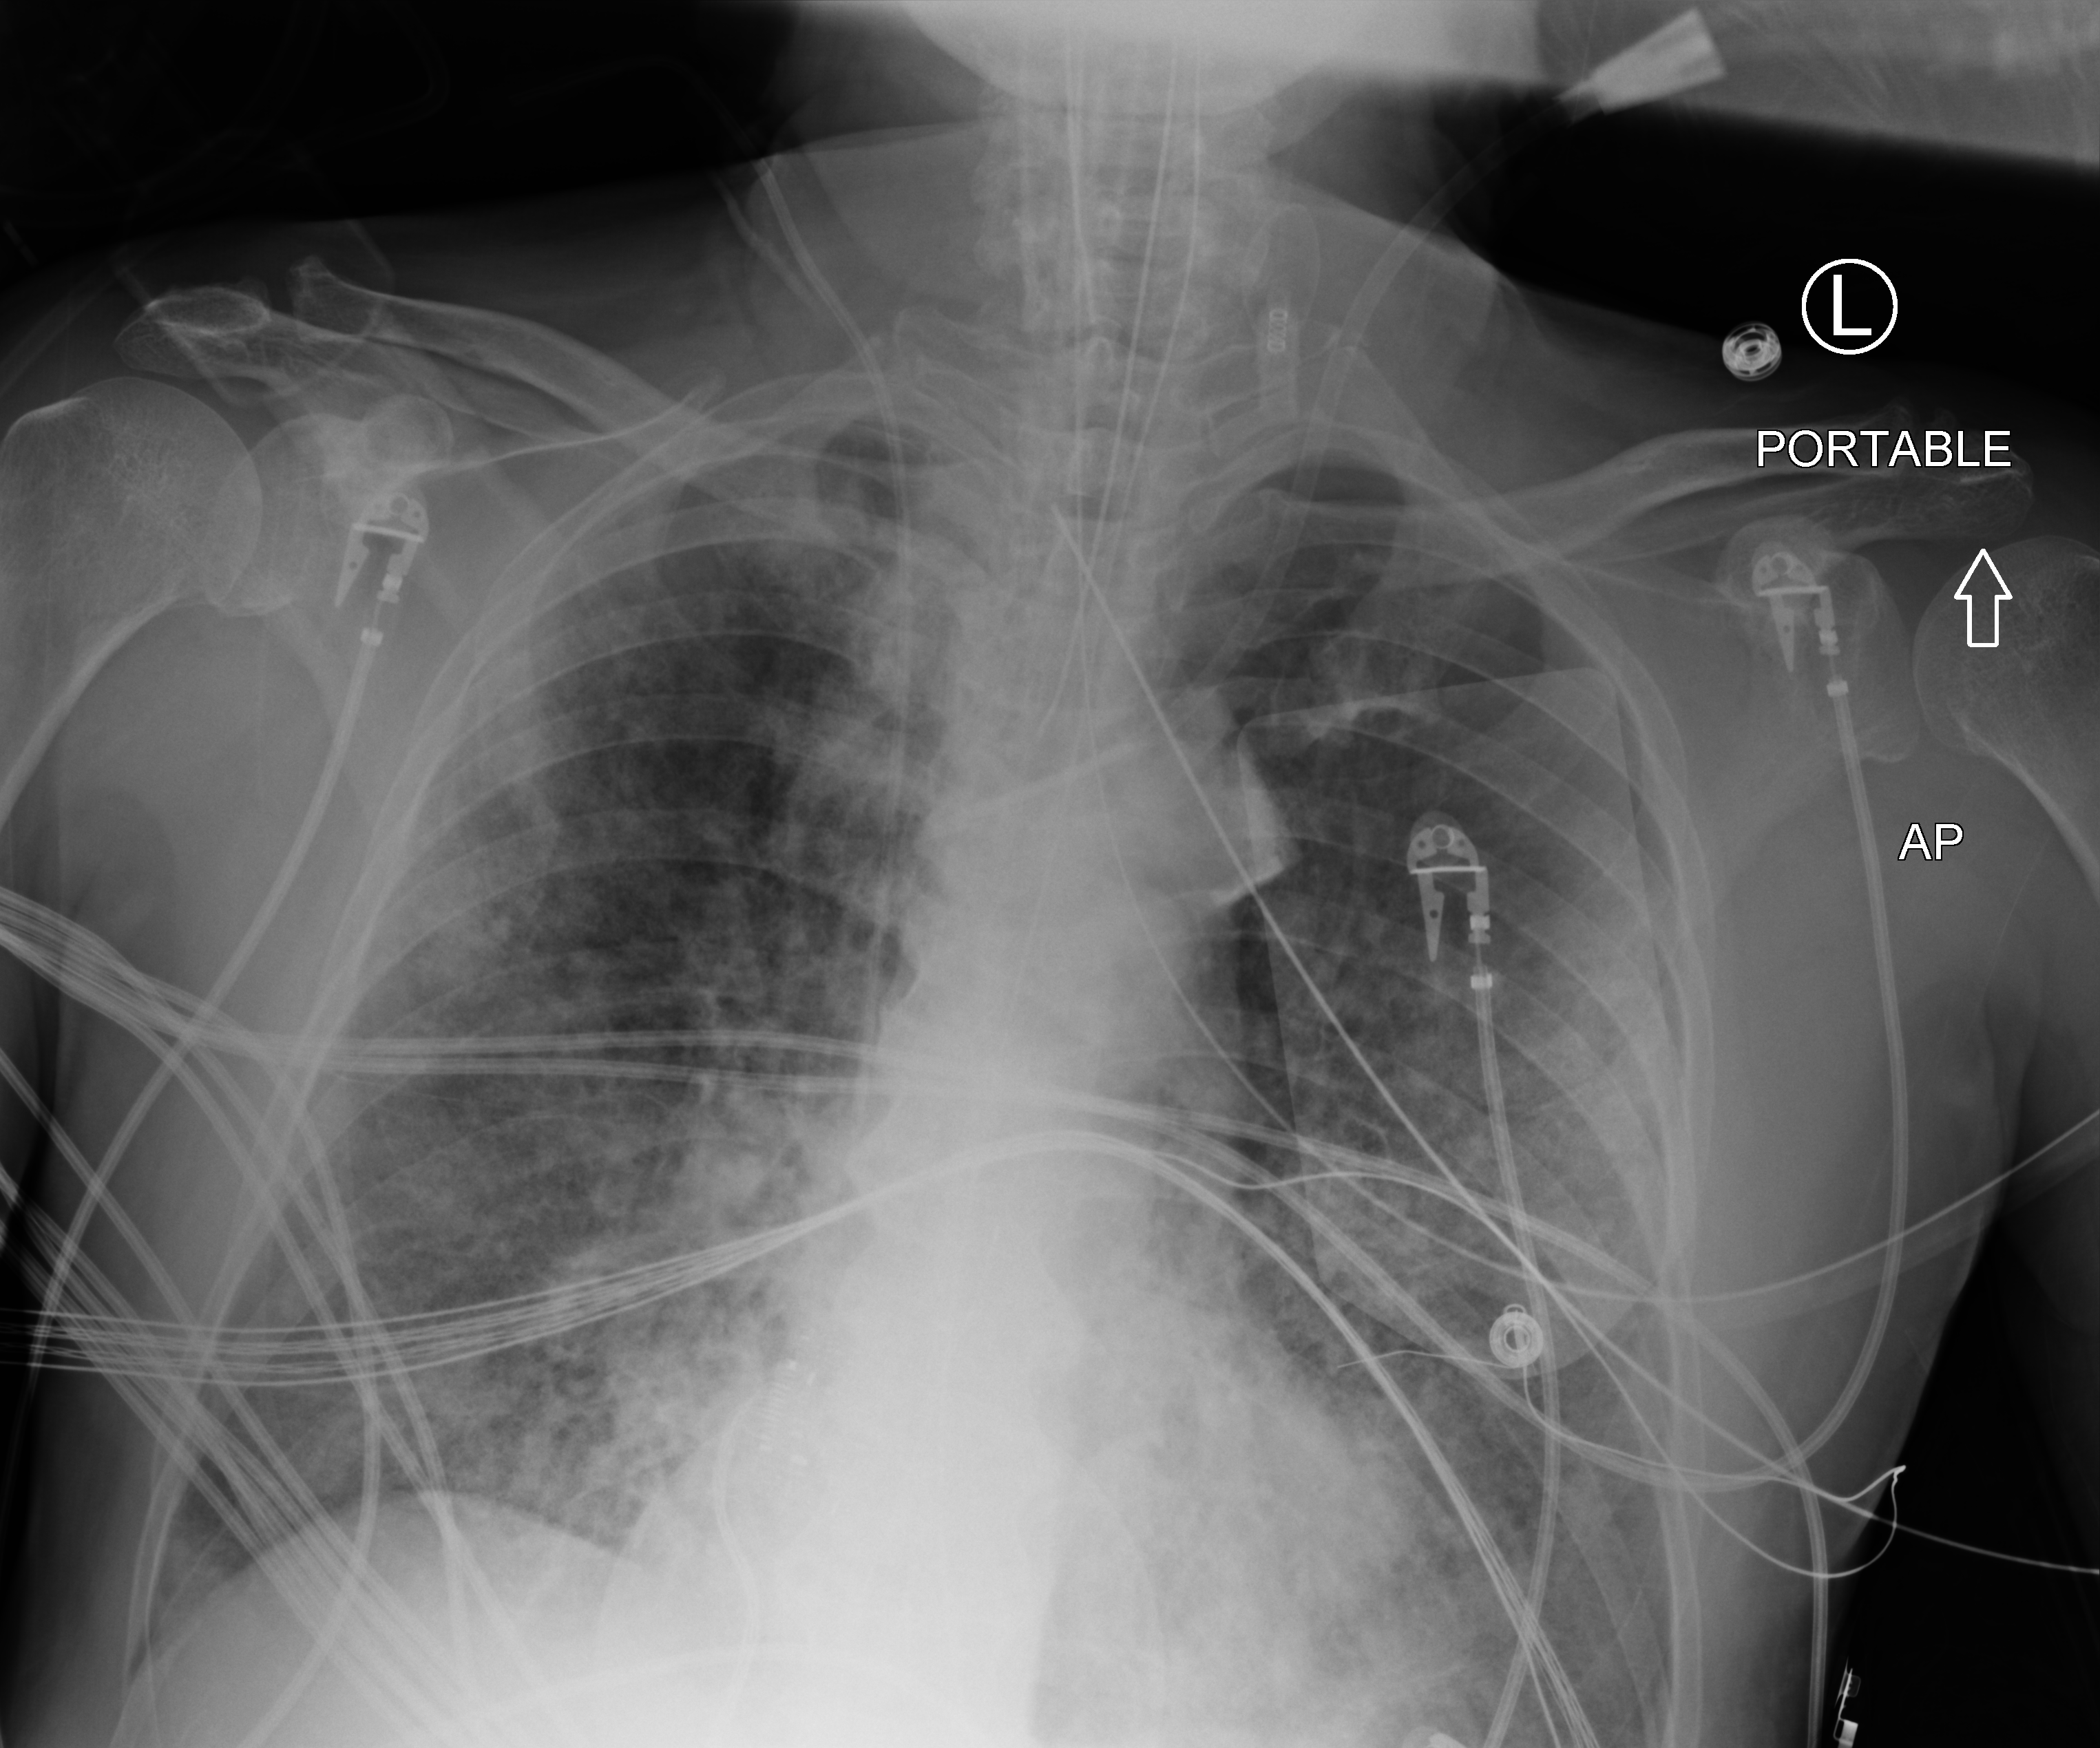
Bedside chest radiograph (computed radiography), anteroposterior (AP) projection. Male patient hospitalised with COVID-19, age 60–74 years.
Hospital-stay facts (about this admission, not read from this image; timing relative to this image not recorded):
- diabetes (admission record): no
- hypertension (admission record): yes